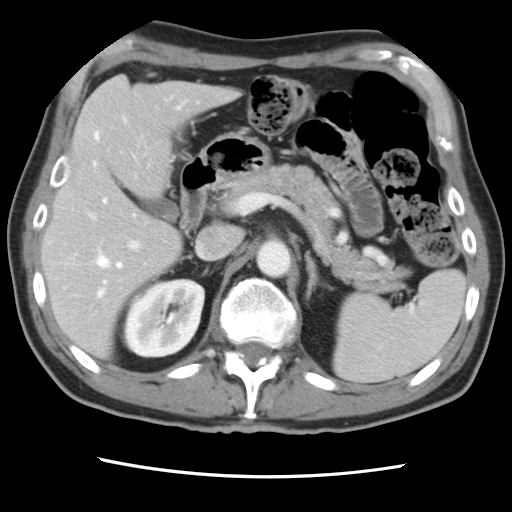
Contrast-enhanced abdominal CT, one axial slice. Slice 48 of 83 in the series (ordered by position). 120 kVp. Intravenous contrast given. Soft-tissue window (W 400 / L 40 HU). 5 mm slice thickness. 512 × 512 image matrix. Male patient, age 69 years. From the clinical record (not read from this slice): diagnosis: colorectal cancer liver metastases, imaged before liver resection; multiple liver metastases: yes; largest metastasis: 3.5 cm; disease in both lobes: no.
Annotated regions visible in this slice (outlined manually by an expert reader):
- hepatic veins: box from (x=94, y=106) to (x=181, y=296) px
- liver: (x=44, y=76)–(x=236, y=356)
- planned liver remnant (the part of the liver to remain after resection): (x=44, y=136)–(x=183, y=356)
- portal vein (with intrahepatic branches): (x=69, y=212)–(x=141, y=260)